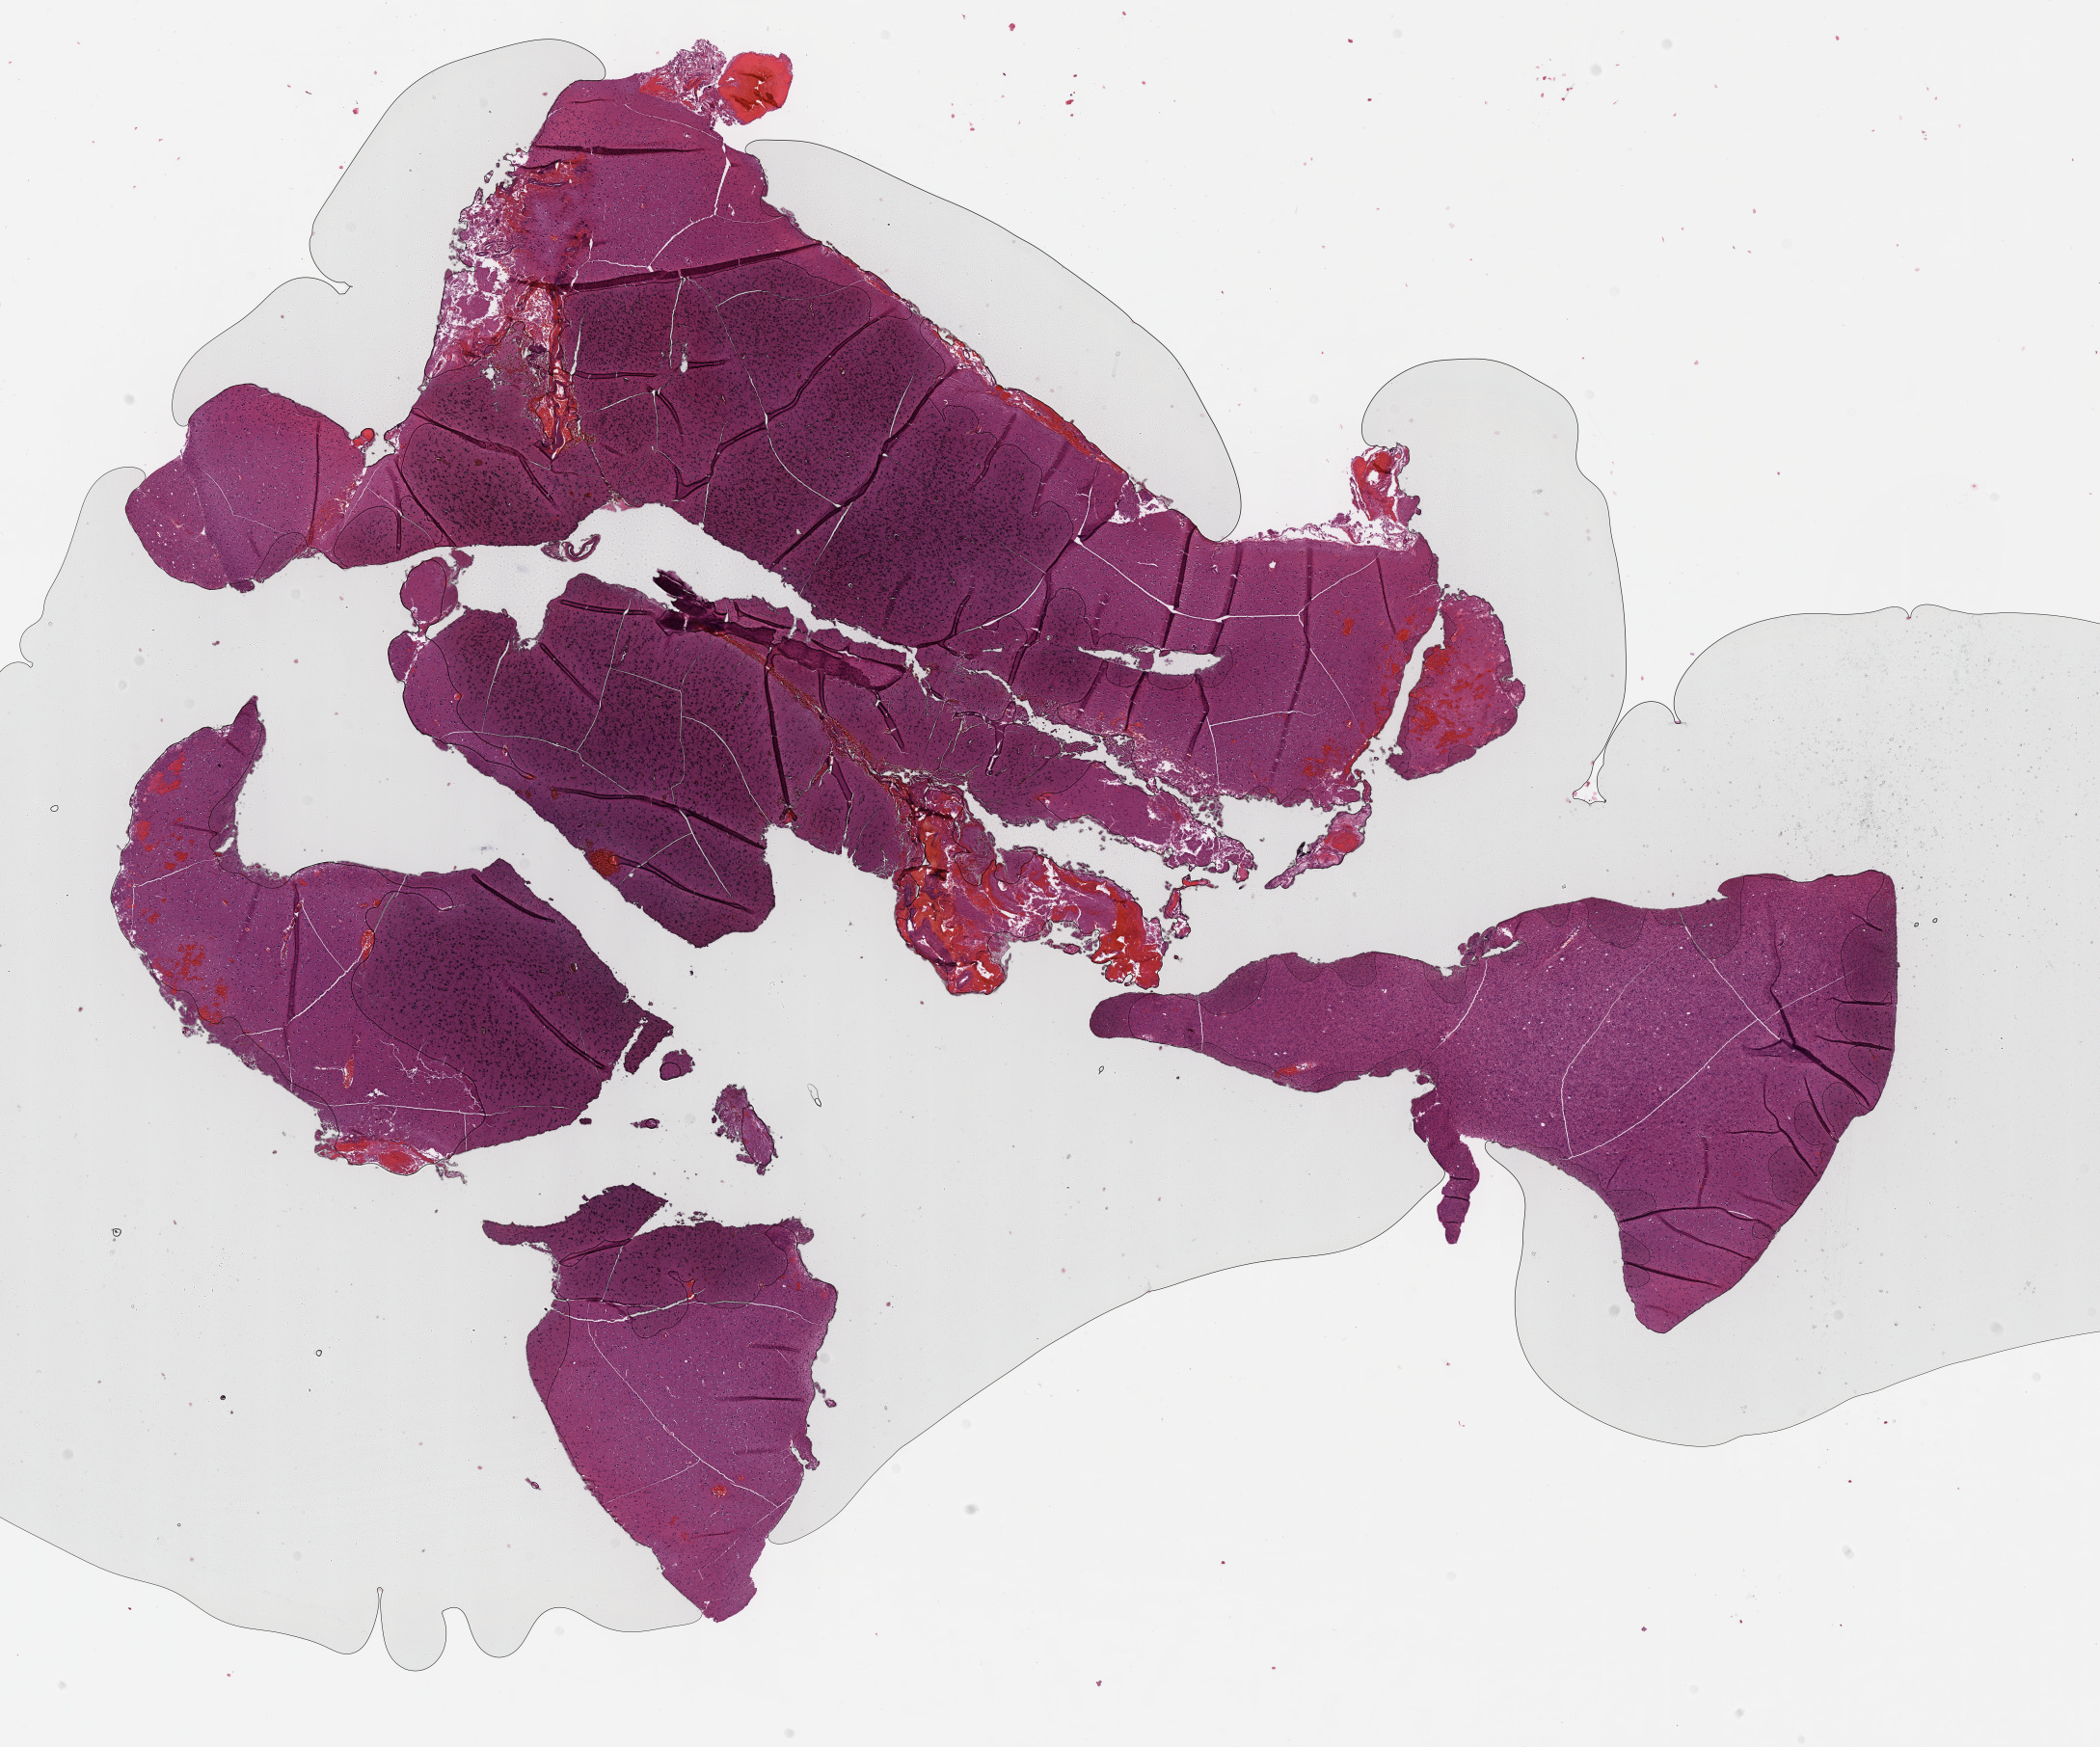
Whole-slide histology image, Hematoxylin and eosin (H&E) stained — low-resolution overview of the scanned area, about 17.6 x 14.7 mm (from a 40x scan), formalin-fixed paraffin-embedded (FFPE) diagnostic section, sample: primary tumour, brain. Female patient; age at initial diagnosis 29 years. Histologic grade: G2 (moderately differentiated).
Histologic diagnosis: Mixed glioma (cerebrum).